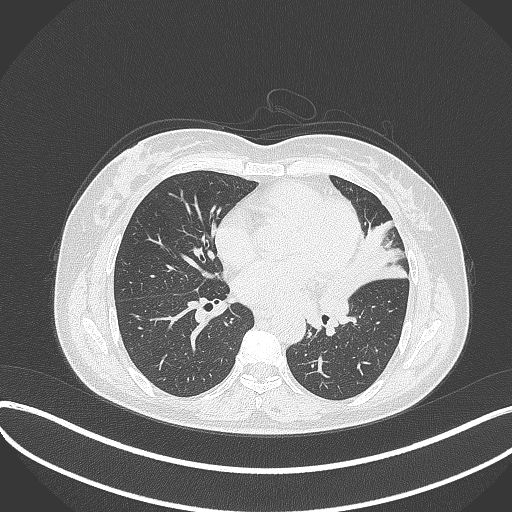
Chest CT, one axial slice. Slice 165 of 373 in the series (ordered by position). Reconstruction kernel B70f. Lung window (W 1500 / L -600 HU). 512 × 512 image matrix, field of view 400 × 400 mm. Patient: female, 54 years. From the clinical record (not read from this slice): clinical TNM (as recorded): T2a N1 M0.
Outlined on this slice (bounding box drawn by a radiologist):
- lung tumour (recorded histology: small cell carcinoma): bounding box (x1, y1, x2, y2) in pixels: (307, 265, 355, 330)